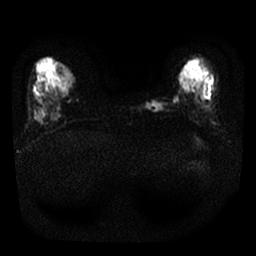
Breast MRI, one axial slice. Position 5 of 24 along the scan axis. Diffusion-weighted series; image 2 of 4 stored at this slice position (different b-values; order by instance number). 1.5 T. 256 × 256 image matrix, field of view 300 × 300 mm. Female patient.
Outlined on this slice (outlined manually by an expert reader):
- tumour on diffusion-weighted imaging: bounding box [x1, y1, x2, y2] px = [146, 102, 161, 113]